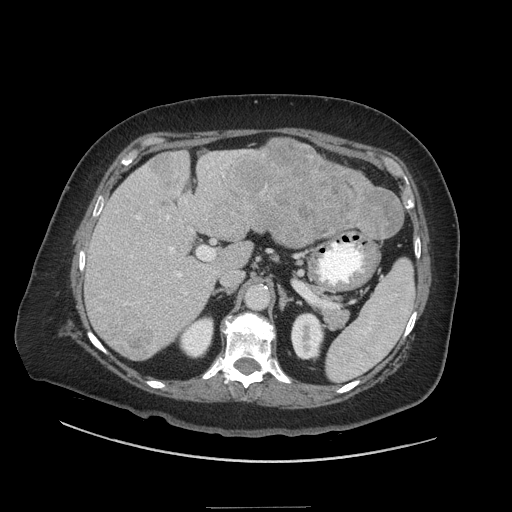
Contrast-enhanced abdominal CT (liver protocol), one axial slice; position 24 of 81 along the scan axis; reconstruction kernel STANDARD; soft-tissue window (W 400 / L 40 HU); 2.5 mm slice thickness; 512 × 512 image matrix. Case-level facts recorded for this patient, not image findings: diagnosis: hepatocellular carcinoma (patient treated with transarterial chemoembolisation; whether this scan precedes or follows treatment is not stated here); TNM stage (as recorded): Stage-II; Child-Pugh class: A; tumour differentiation: moderately differentiated; tumour nodularity: multinodular.
Outlined on this slice (semi-automatically segmented with operator editing):
- liver parenchyma outside the tumour (the mass and vessels are separate outlines, so this box may not span the whole liver): bounding box (x1, y1, x2, y2) in pixels: (85, 138, 390, 360)
- mass: (122, 141, 402, 357)
- liver vessels: (98, 166, 215, 310)